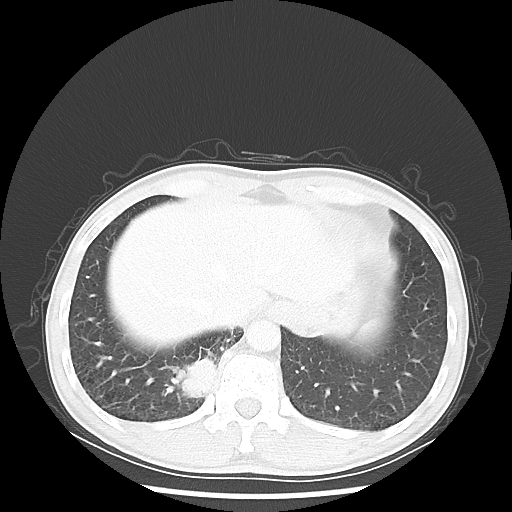
Chest CT, one axial slice. Position 8 of 58 along the scan axis. Reconstruction kernel LUNG. 100 kVp. Lung window (W 1500 / L -600 HU). 5 mm slice thickness. 512 × 512 image matrix. Patient: male, 56 years. Case-level facts recorded for this patient, not image findings: clinical TNM (as recorded): T2 N1 M1; histopathological grade: G1.
Outlined on this slice (rectangle marked by the reading radiologist):
- lung tumour (recorded histology: adenocarcinoma): bounding box [x1, y1, x2, y2] px = [175, 348, 216, 400]